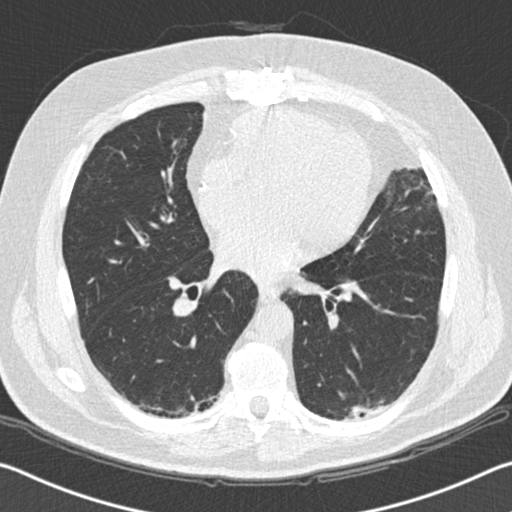
Axial slice from a low-dose chest CT screening exam, second screening round (one year after baseline), lung window (W 1500 / L -600 HU), standard (soft-tissue) reconstruction kernel (B30f), slice 89 of 172 in the series, 512 × 512 image matrix, field of view 340 × 340 mm. Male, age 65 years at enrolment. Former smoker at enrolment.
• Lesion marked by an expert reader, bounding box [x1, y1, x2, y2] px = [325, 390, 398, 435].
• The exam's reader record, not a measurement of the box and not confirmed to be the same lesion: non-calcified nodule or mass ≥4 mm, left lower lobe, 19 × 11 mm, spiculated (stellate) margins, soft tissue attenuation, pre-existing on the prior screen: yes; interval growth: yes.
• Official screen result: positive, change unspecified: nodule(s) >= 4 mm or enlarging nodule(s), mass(es), or other non-specific abnormalities suspicious for lung cancer.
• Lung cancer was diagnosed 179 days after this screen: squamous cell carcinoma, NOS, left lower lobe, moderately differentiated (G2), stage IA (AJCC 6th edition), 20 mm at pathology.